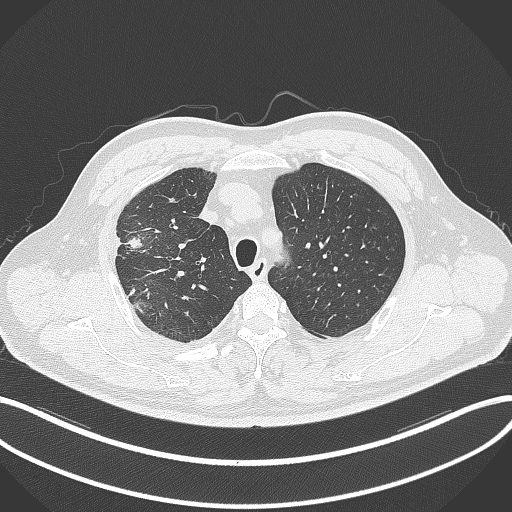
Chest CT, one axial slice. Position 273 of 348 along the scan axis. 120 kVp. Lung window (W 1500 / L -600 HU). 1 mm slice thickness. 512 × 512 image matrix, field of view 400 × 400 mm. Patient: male, 55 years. From the clinical record (not read from this slice): clinical TNM (as recorded): T3 N2 M1.
Structures marked on this image (rectangle marked by the reading radiologist):
- lung tumour (recorded histology: adenocarcinoma): bounding box [x1, y1, x2, y2] px = [124, 234, 146, 252]